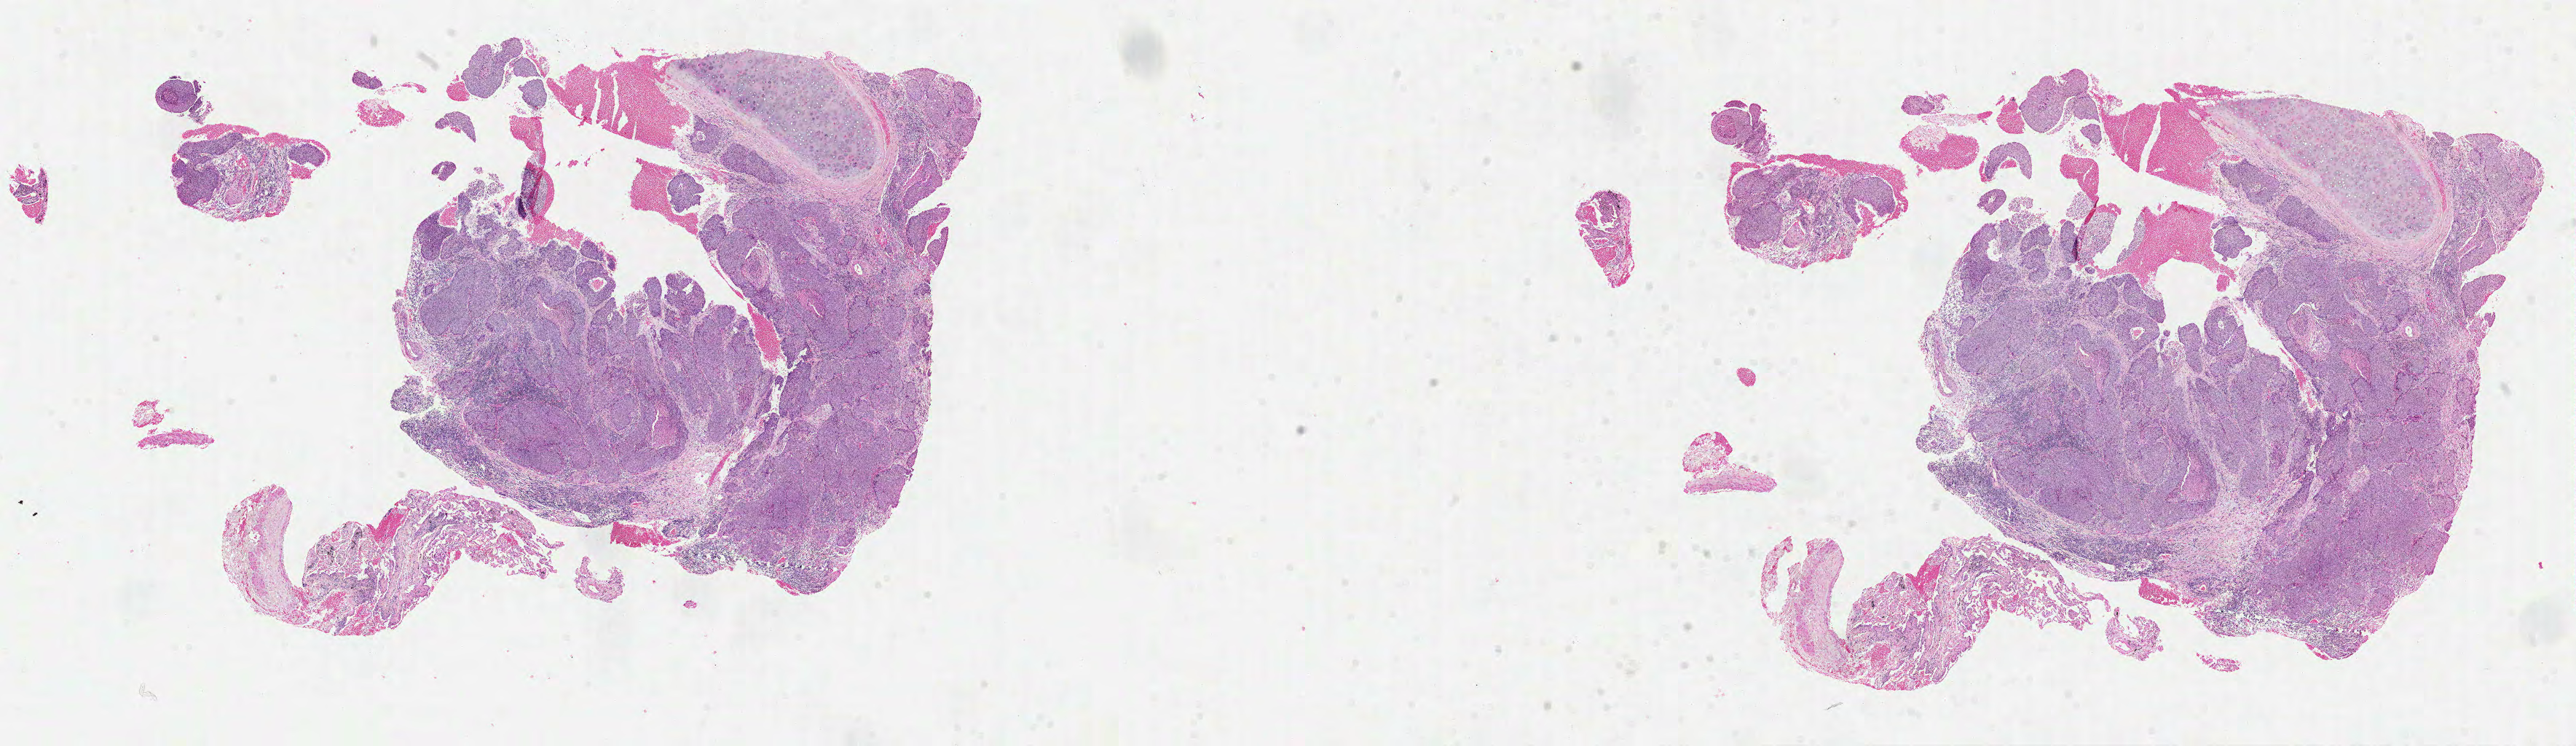
H&E-stained whole-slide image — whole scanned area (about 28.5 x 8.3 mm, acquisition: 40x scan) shown as a low-resolution overview; FFPE section; sample: primary tumour, lung. Male patient; age at initial diagnosis 64 years.
• AJCC pathologic stage: IIIB (6th edition)
• laterality: left
• pathologic diagnosis: Squamous cell carcinoma, NOS (upper lobe, lung)